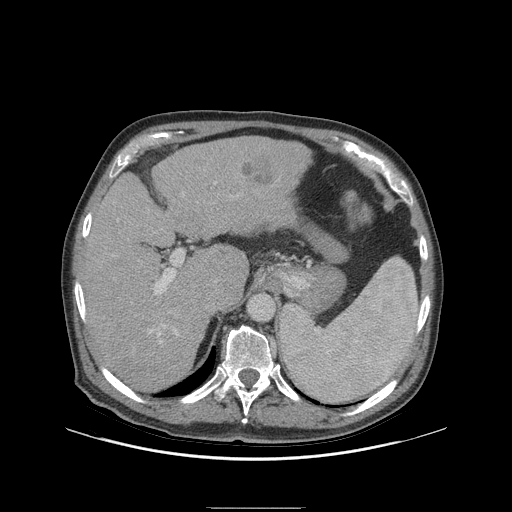
Contrast-enhanced abdominal CT (liver protocol), one axial slice. Slice 65 of 105 in the series (ordered by position). Reconstruction kernel STANDARD. Soft-tissue window (W 400 / L 40 HU). 2.5 mm slice thickness. 512 × 512 image matrix. Case-level facts recorded for this patient, not image findings: diagnosis: hepatocellular carcinoma (patient treated with transarterial chemoembolisation; whether this scan precedes or follows treatment is not stated here); TNM stage (as recorded): Stage-I; Child-Pugh class: A; tumour nodularity: uninodular; tumour size: 5.1 cm.
Annotated regions visible in this slice (semi-automatic segmentation, software-assisted and operator-edited):
- liver parenchyma outside the tumour (the mass and vessels are separate outlines, so this box may not span the whole liver): bounding box [x1, y1, x2, y2] px = [80, 136, 308, 392]
- mass: [242, 149, 278, 184]
- liver vessels: [149, 182, 216, 343]